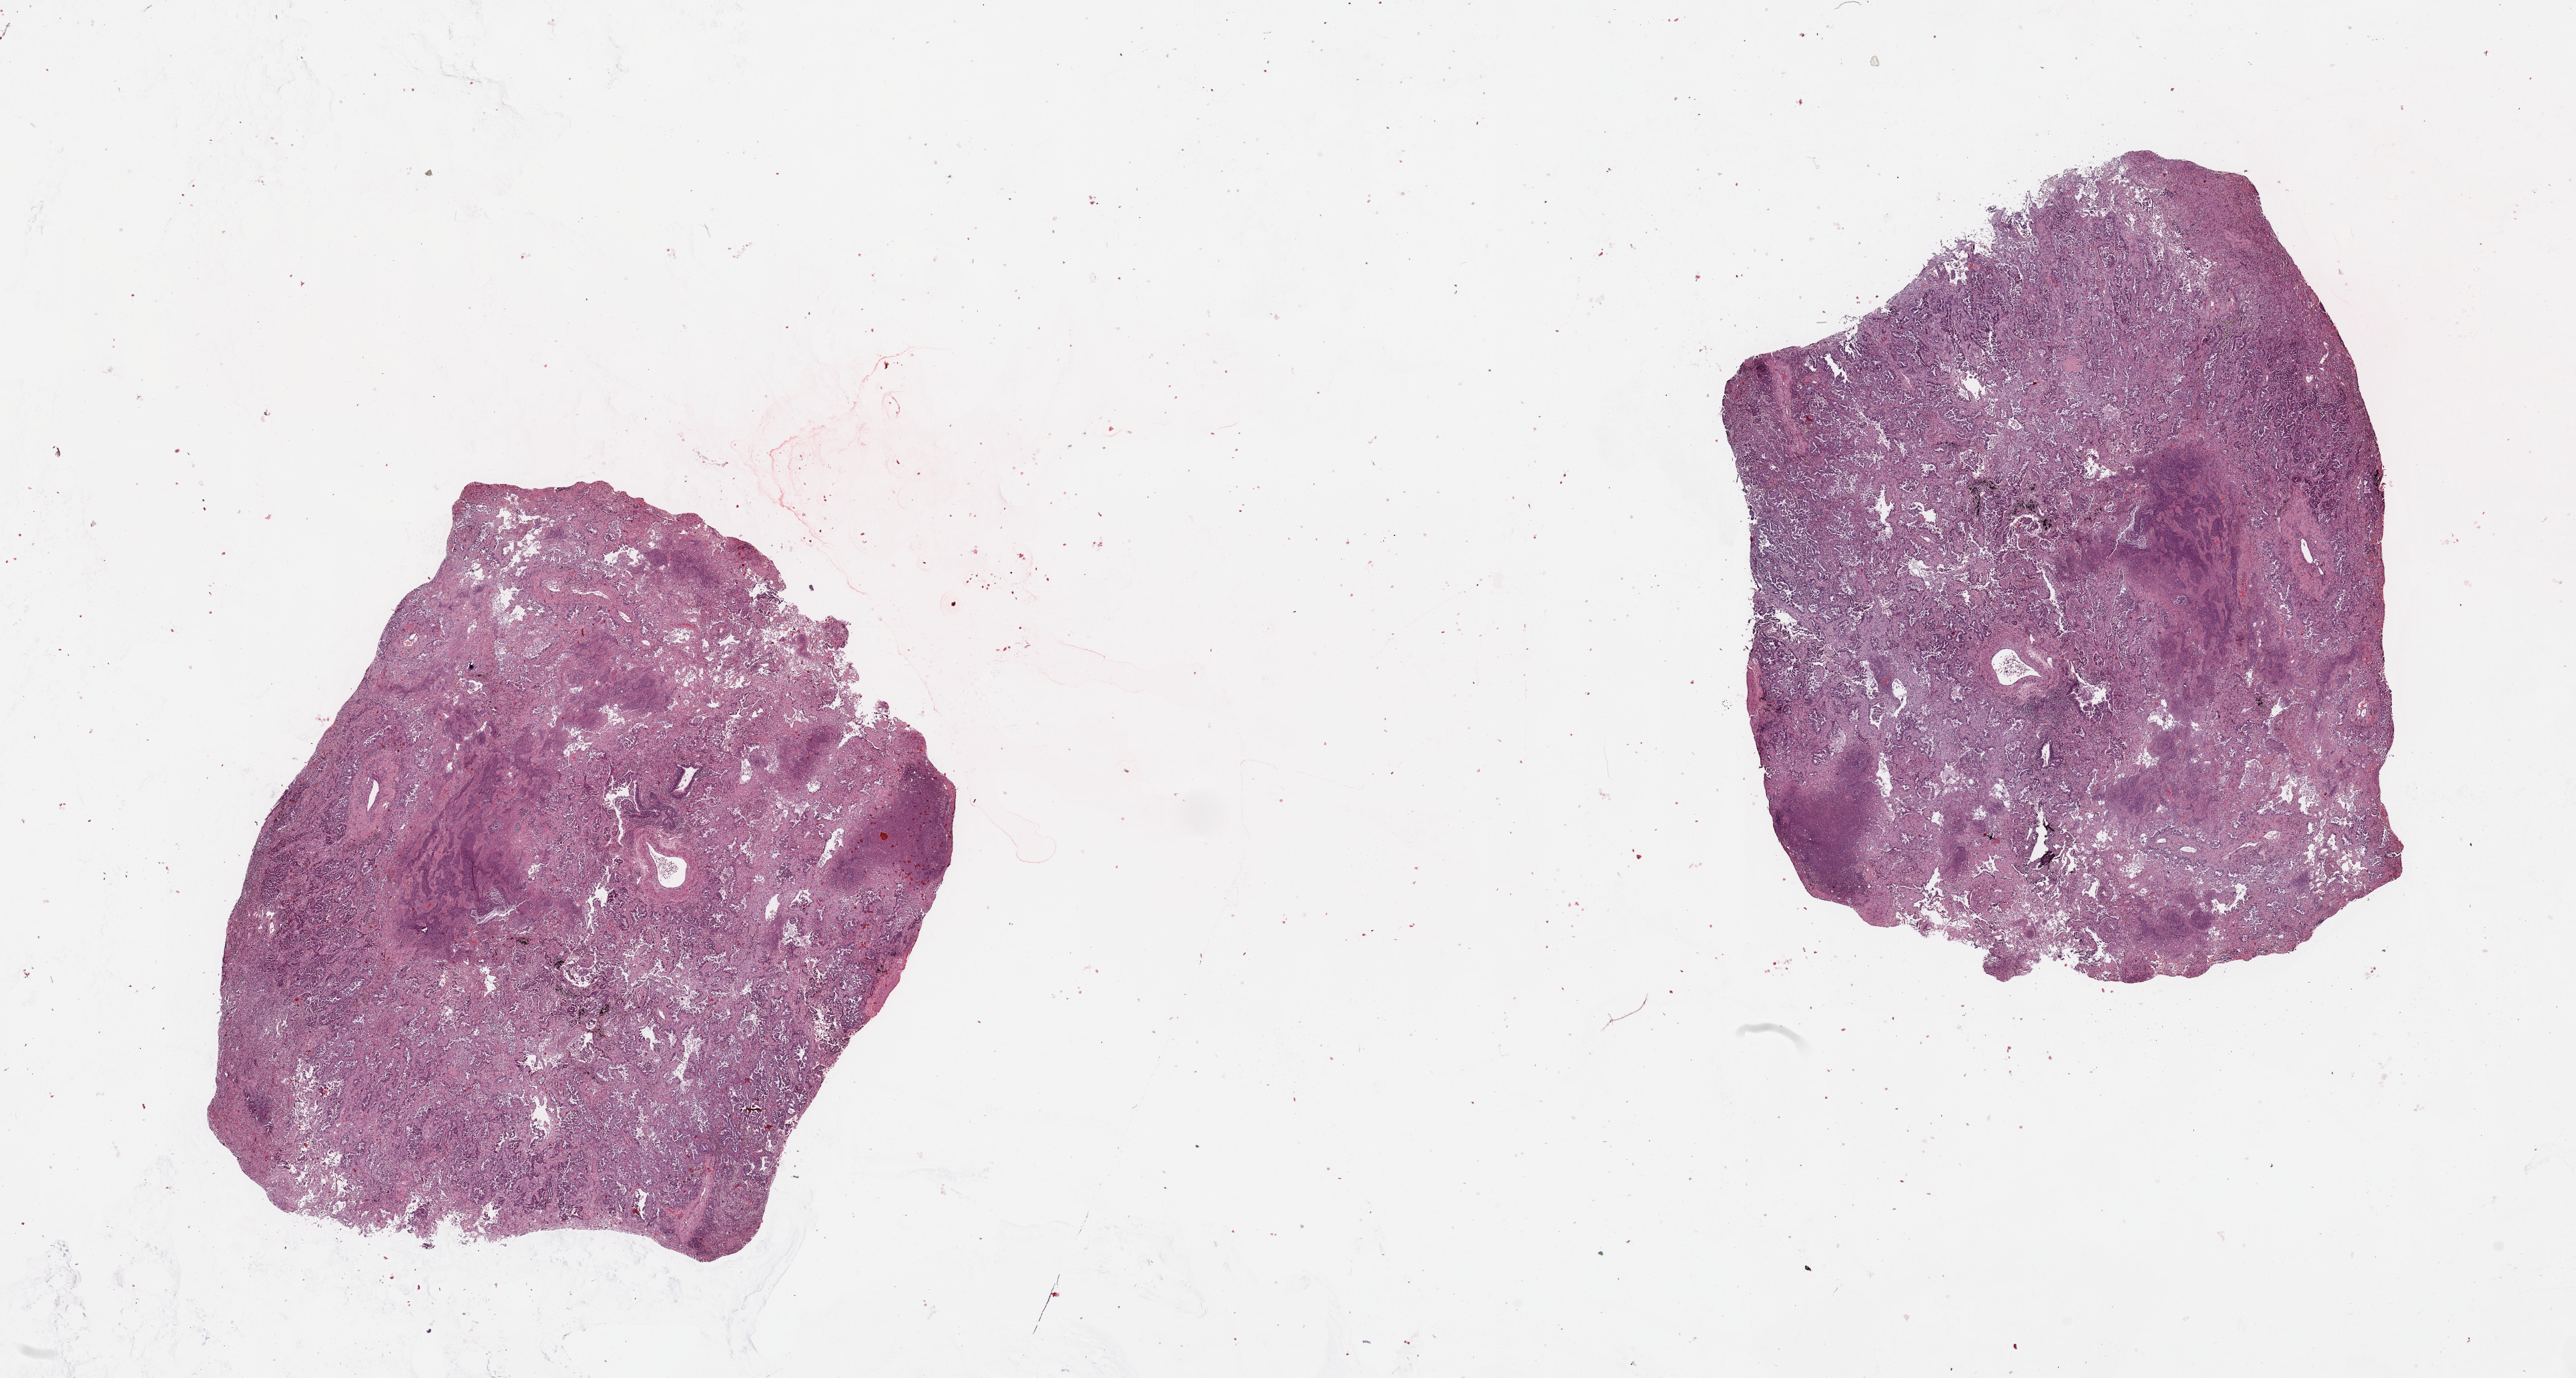
Digitized Hematoxylin and eosin (H&E) stained tissue section (whole slide) — whole scanned area (about 30.5 x 16.3 mm, from a 20x scan) shown as a low-resolution overview; tumour tissue sample, lung. 59-year-old male patient. Histologic grade: G3 (poorly differentiated).
• histologic diagnosis: Adenocarcinoma, NOS
• primary tumour site (as recorded): right upper lobe
• AJCC pathologic stage: IB